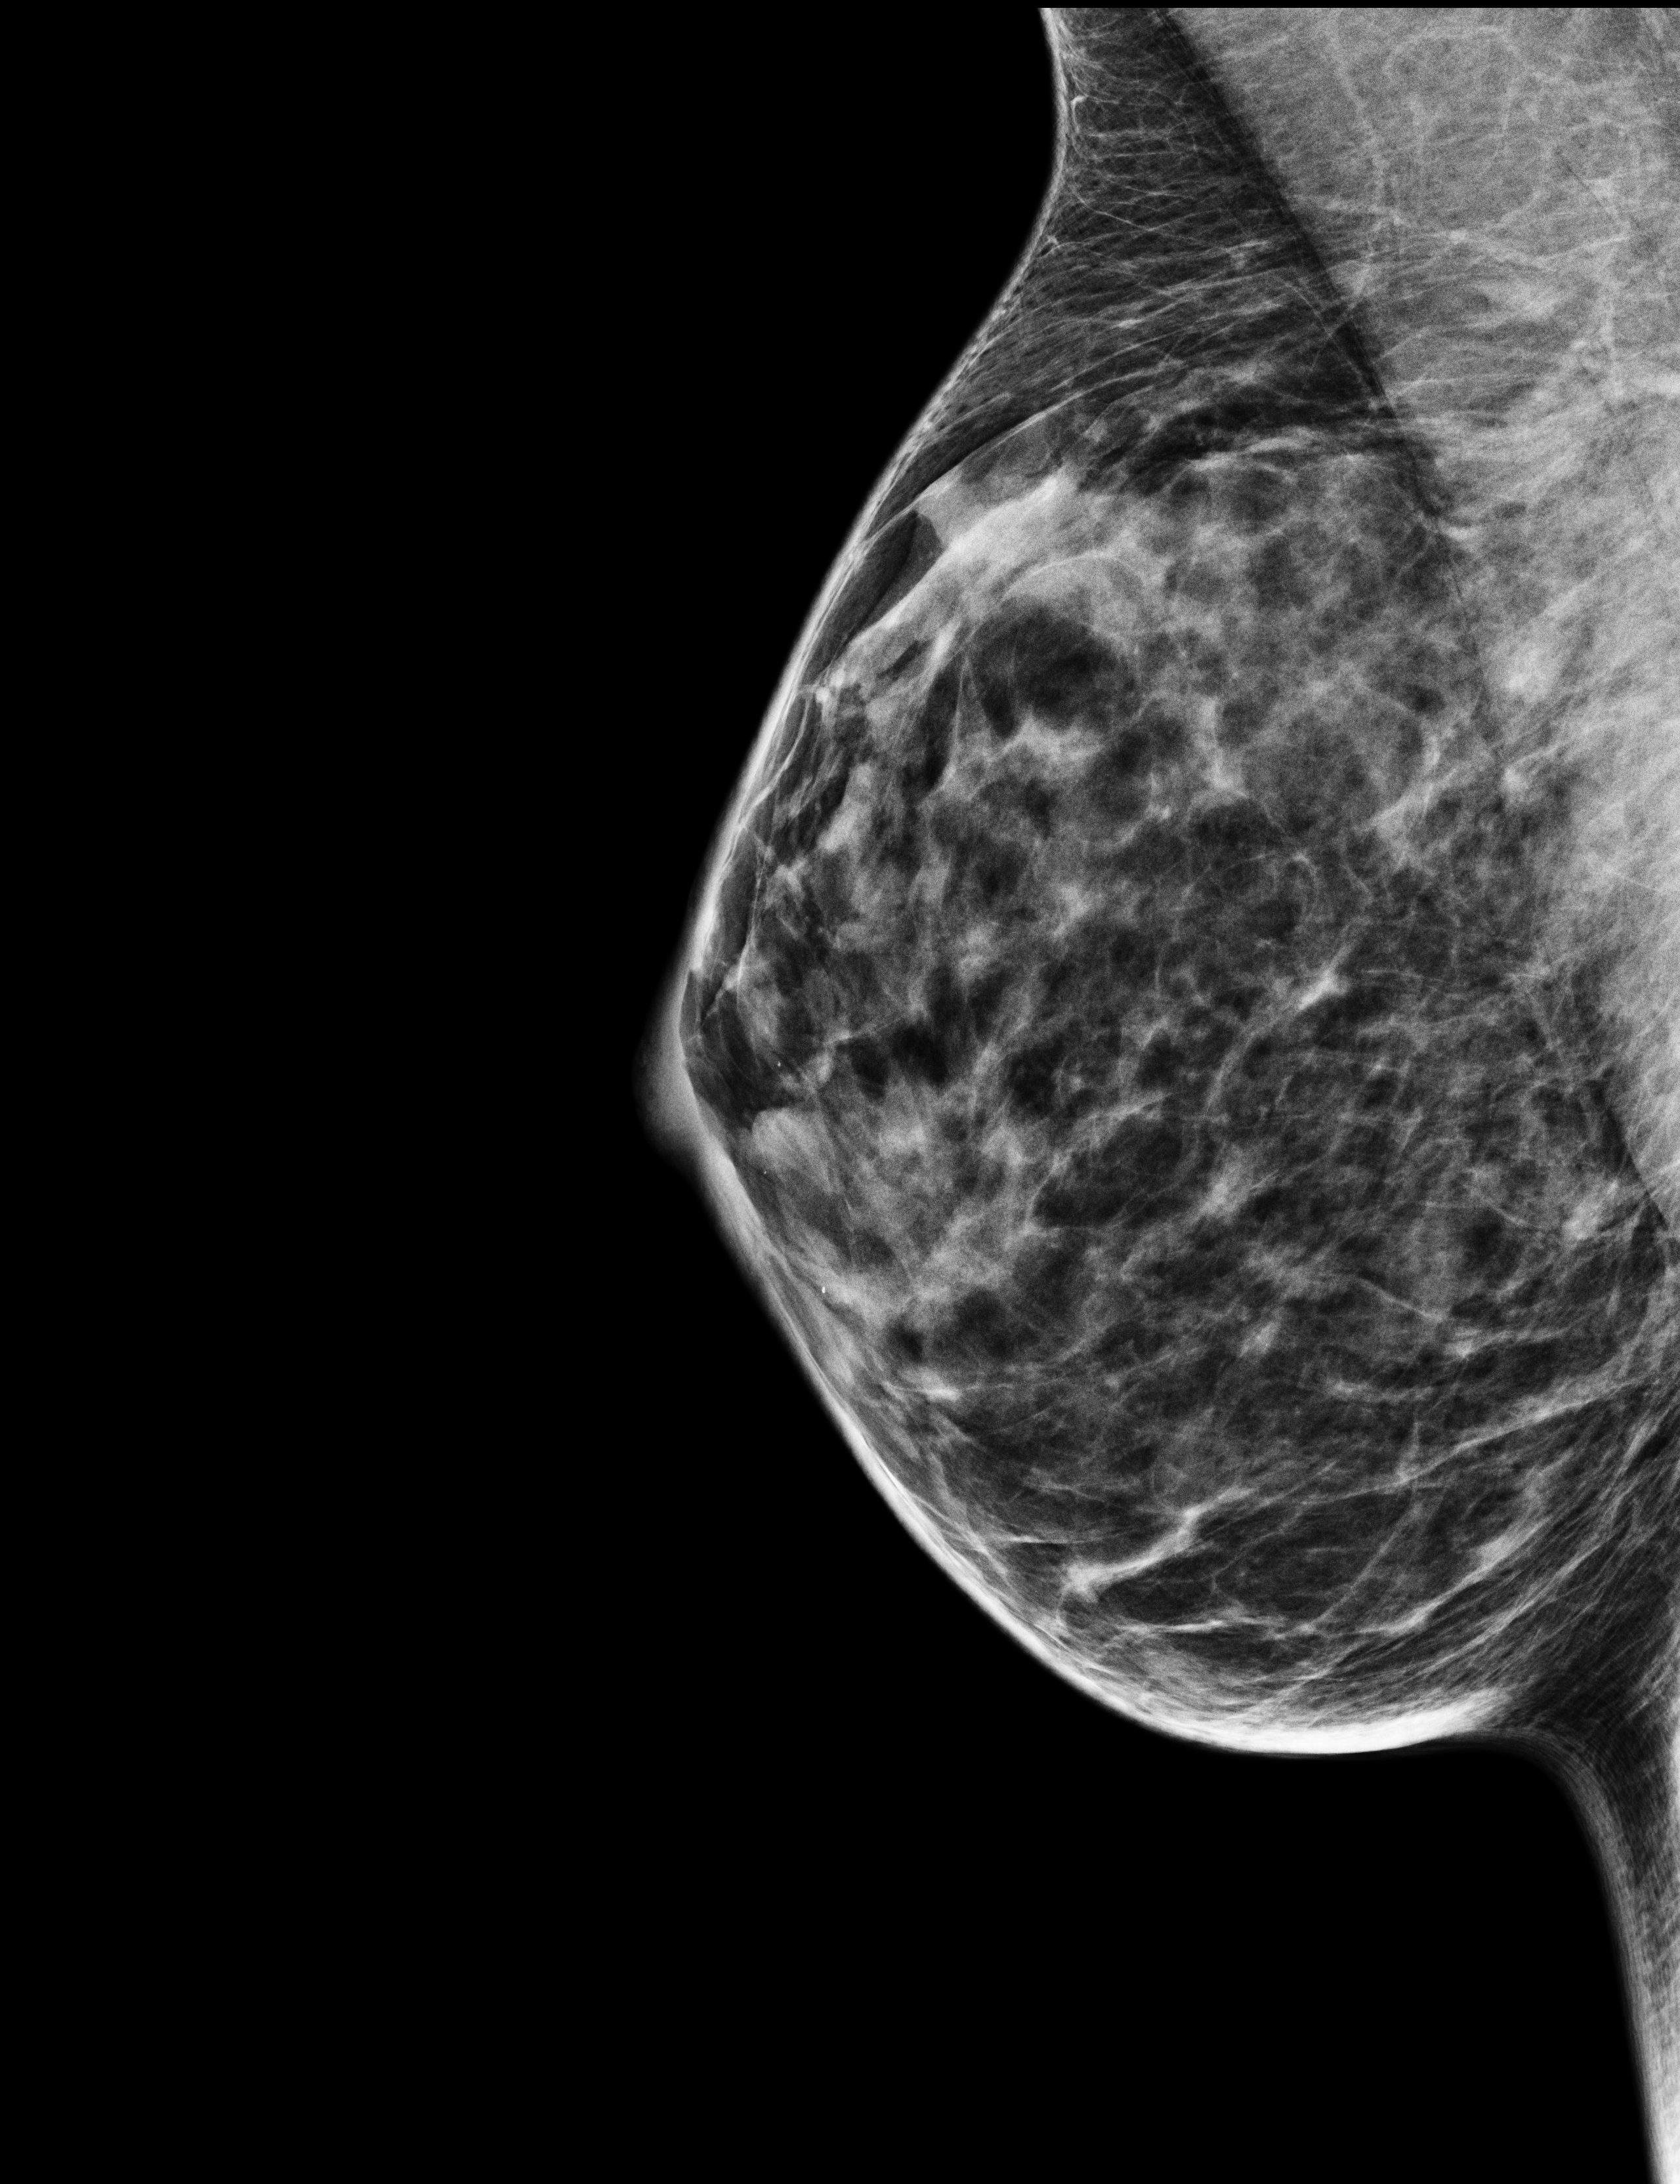
Full-field digital mammogram (FFDM), right breast, MLO view, screening examination. Patient aged 44 years (female).
- breast density at the screening exam (both breasts): heterogeneously dense (BI-RADS density category c)
- final BI-RADS category for the screening round (tomosynthesis exam, both breasts): category 2
- recall: recalled for additional imaging after this screen